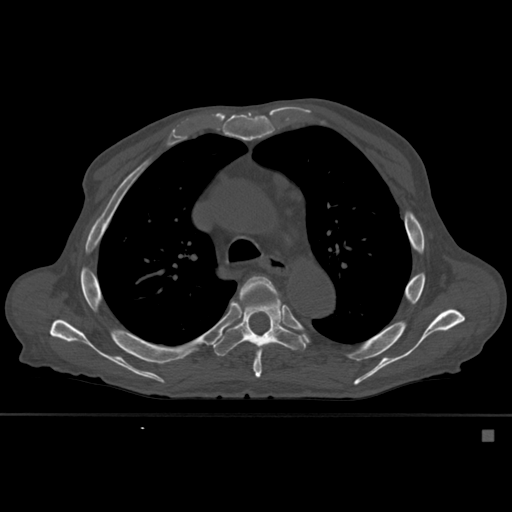
CT including the spine, one axial slice. Slice 391 of 527 in the series (ordered by position). Bone window (W 1800 / L 400 HU). 1.5 mm slice thickness. 512 × 512 image matrix, field of view 373 × 373 mm. Patient: male, 78 years. Case-level facts recorded for this patient, not image findings: primary cancer: prostate.
Outlined on this slice (semi-automatically segmented with operator editing):
- T5 vertebra: bounding box <239,276,280,378> (left, top, right, bottom; pixels)
- T6 vertebra: <213,278,304,357>